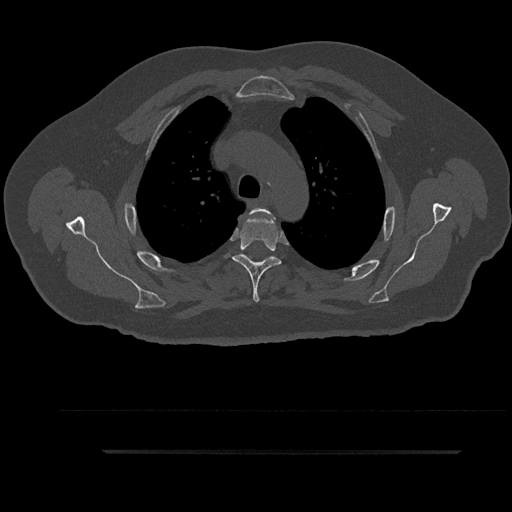
CT including the spine, one axial slice; position 673 of 797 along the scan axis; reconstruction kernel Br40s/3; 120 kVp; bone window (W 1800 / L 400 HU); 0.5 mm slice thickness; 512 × 512 image matrix. Patient: male, 63 years. From the clinical record (not read from this slice): primary cancer: renal.
Outlined on this slice (semi-automatically segmented with operator editing):
- T3 vertebra: bounding box <247,207,273,264> (left, top, right, bottom; pixels)
- T4 vertebra: <224,212,281,302>